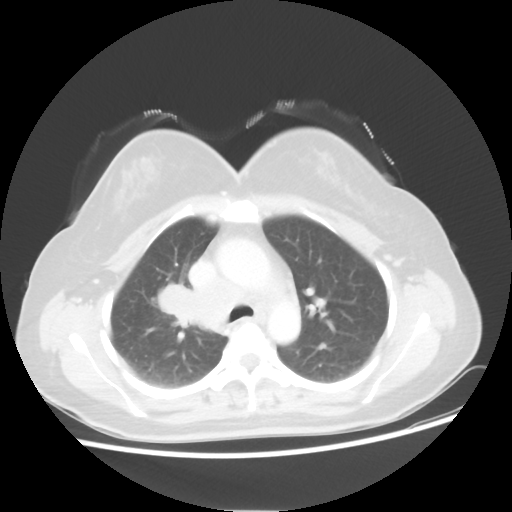
Chest CT, one axial slice; position 35 of 50 along the scan axis; 100 kVp; lung window (W 1500 / L -600 HU); 5 mm slice thickness; 512 × 512 image matrix. Female patient, age 40 years. Case-level facts recorded for this patient, not image findings: clinical TNM (as recorded): T1c N3 M0.
Outlined on this slice (rectangle marked by the reading radiologist):
- lung tumour (recorded histology: small cell carcinoma): bounding box <156,277,192,327> (left, top, right, bottom; pixels)